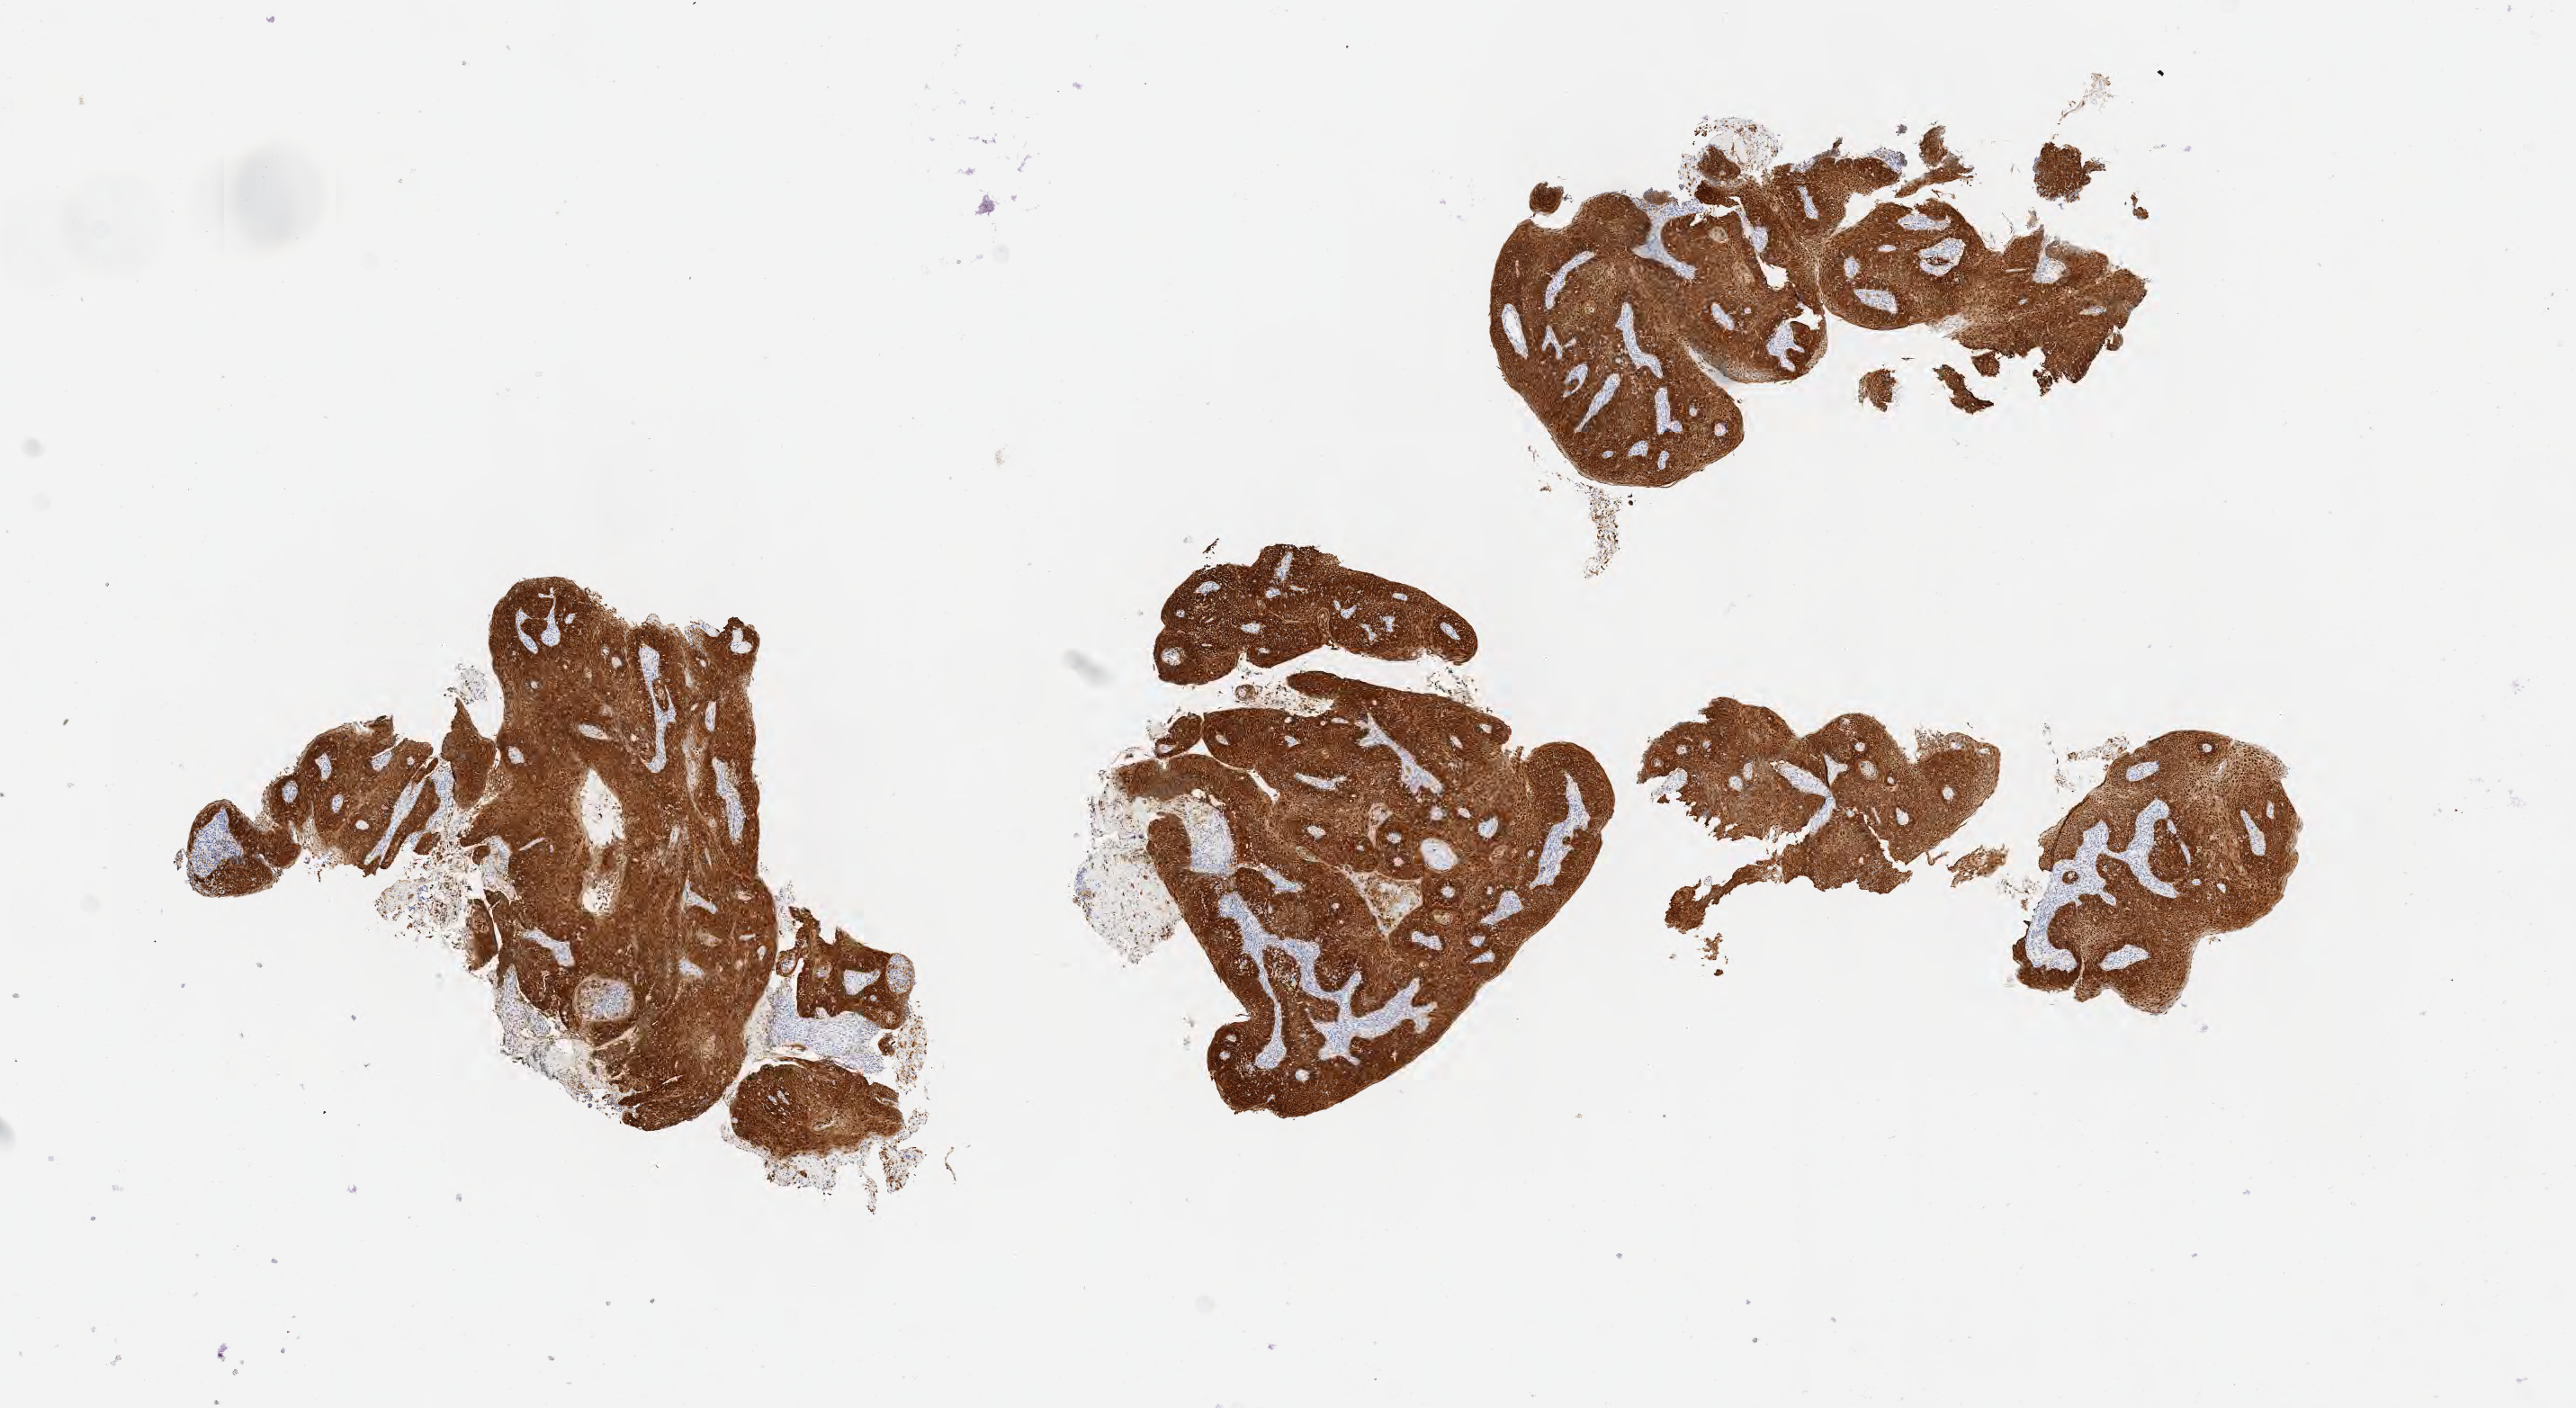
Immunohistochemistry (IHC) whole-slide image stained for p16 (p16INK4a) — shown as a low-resolution overview of the whole scanned area (about 11.6 x 6.3 mm); tumor tissue; anatomic site: cervix. Patient: female, age 48 years.
• histologic diagnosis: Squamous cell carcinoma, keratinizing, NOS